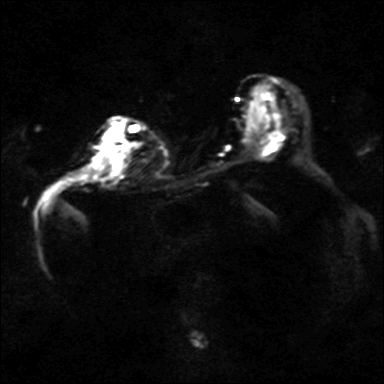
Breast MRI, one axial slice; position 23 of 40 along the scan axis; diffusion-weighted series; image 2 of 4 stored at this slice position (different b-values; order by instance number); 3 T; 384 × 384 image matrix. Female patient.
Structures marked on this image (outlined manually by an expert reader):
- tumour on diffusion-weighted imaging: box from (x=108, y=145) to (x=118, y=151) px